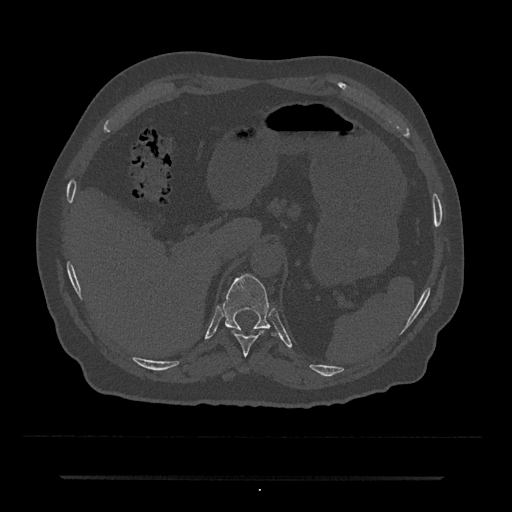
CT including the spine, one axial slice; position 201 of 797 along the scan axis; 120 kVp; bone window (W 1800 / L 400 HU); 0.5 mm slice thickness; 512 × 512 image matrix, field of view 437 × 437 mm. Male patient, age 69 years. Case-level facts recorded for this patient, not image findings: primary cancer: prostate.
Annotated regions visible in this slice (semi-automatically segmented with operator editing):
- T10 vertebra: bounding box [x1, y1, x2, y2] px = [231, 330, 265, 357]
- T11 vertebra: [222, 274, 279, 338]